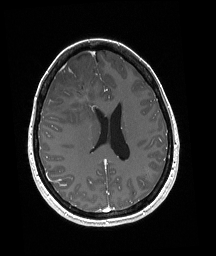
Brain MRI from a brain-tumour surgery series, one axial slice; slice 79 of 192 in the series (ordered by position); T1-weighted post-contrast; 1 mm slice thickness; 216 × 256 image matrix, field of view 211 × 250 mm. From the clinical record (not read from this slice): histopathology: Oligodendroglioma; WHO grade: 3; IDH mutation: yes; tumour location: Right Frontal.
Structures marked on this image (outlined manually by an expert reader):
- tumour: bounding box <58,81,93,99> (left, top, right, bottom; pixels)